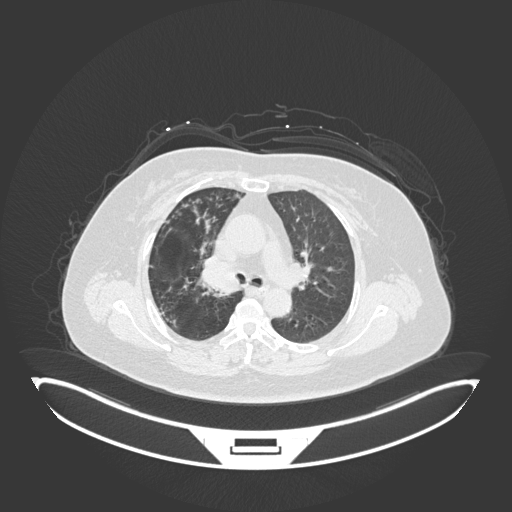
Chest CT, one axial slice; slice 114 of 245 in the series (ordered by position); reconstruction kernel B30f; lung window (W 1500 / L -600 HU); 1 mm slice thickness; 512 × 512 image matrix. Female patient, age 60 years. From the clinical record (not read from this slice): clinical TNM (as recorded): T1c N0 M0; histopathological grade: G1-G2.
Outlined on this slice (bounding box drawn by a radiologist):
- lung tumour (recorded histology: squamous cell carcinoma): bounding box (x1, y1, x2, y2) in pixels: (195, 255, 244, 299)